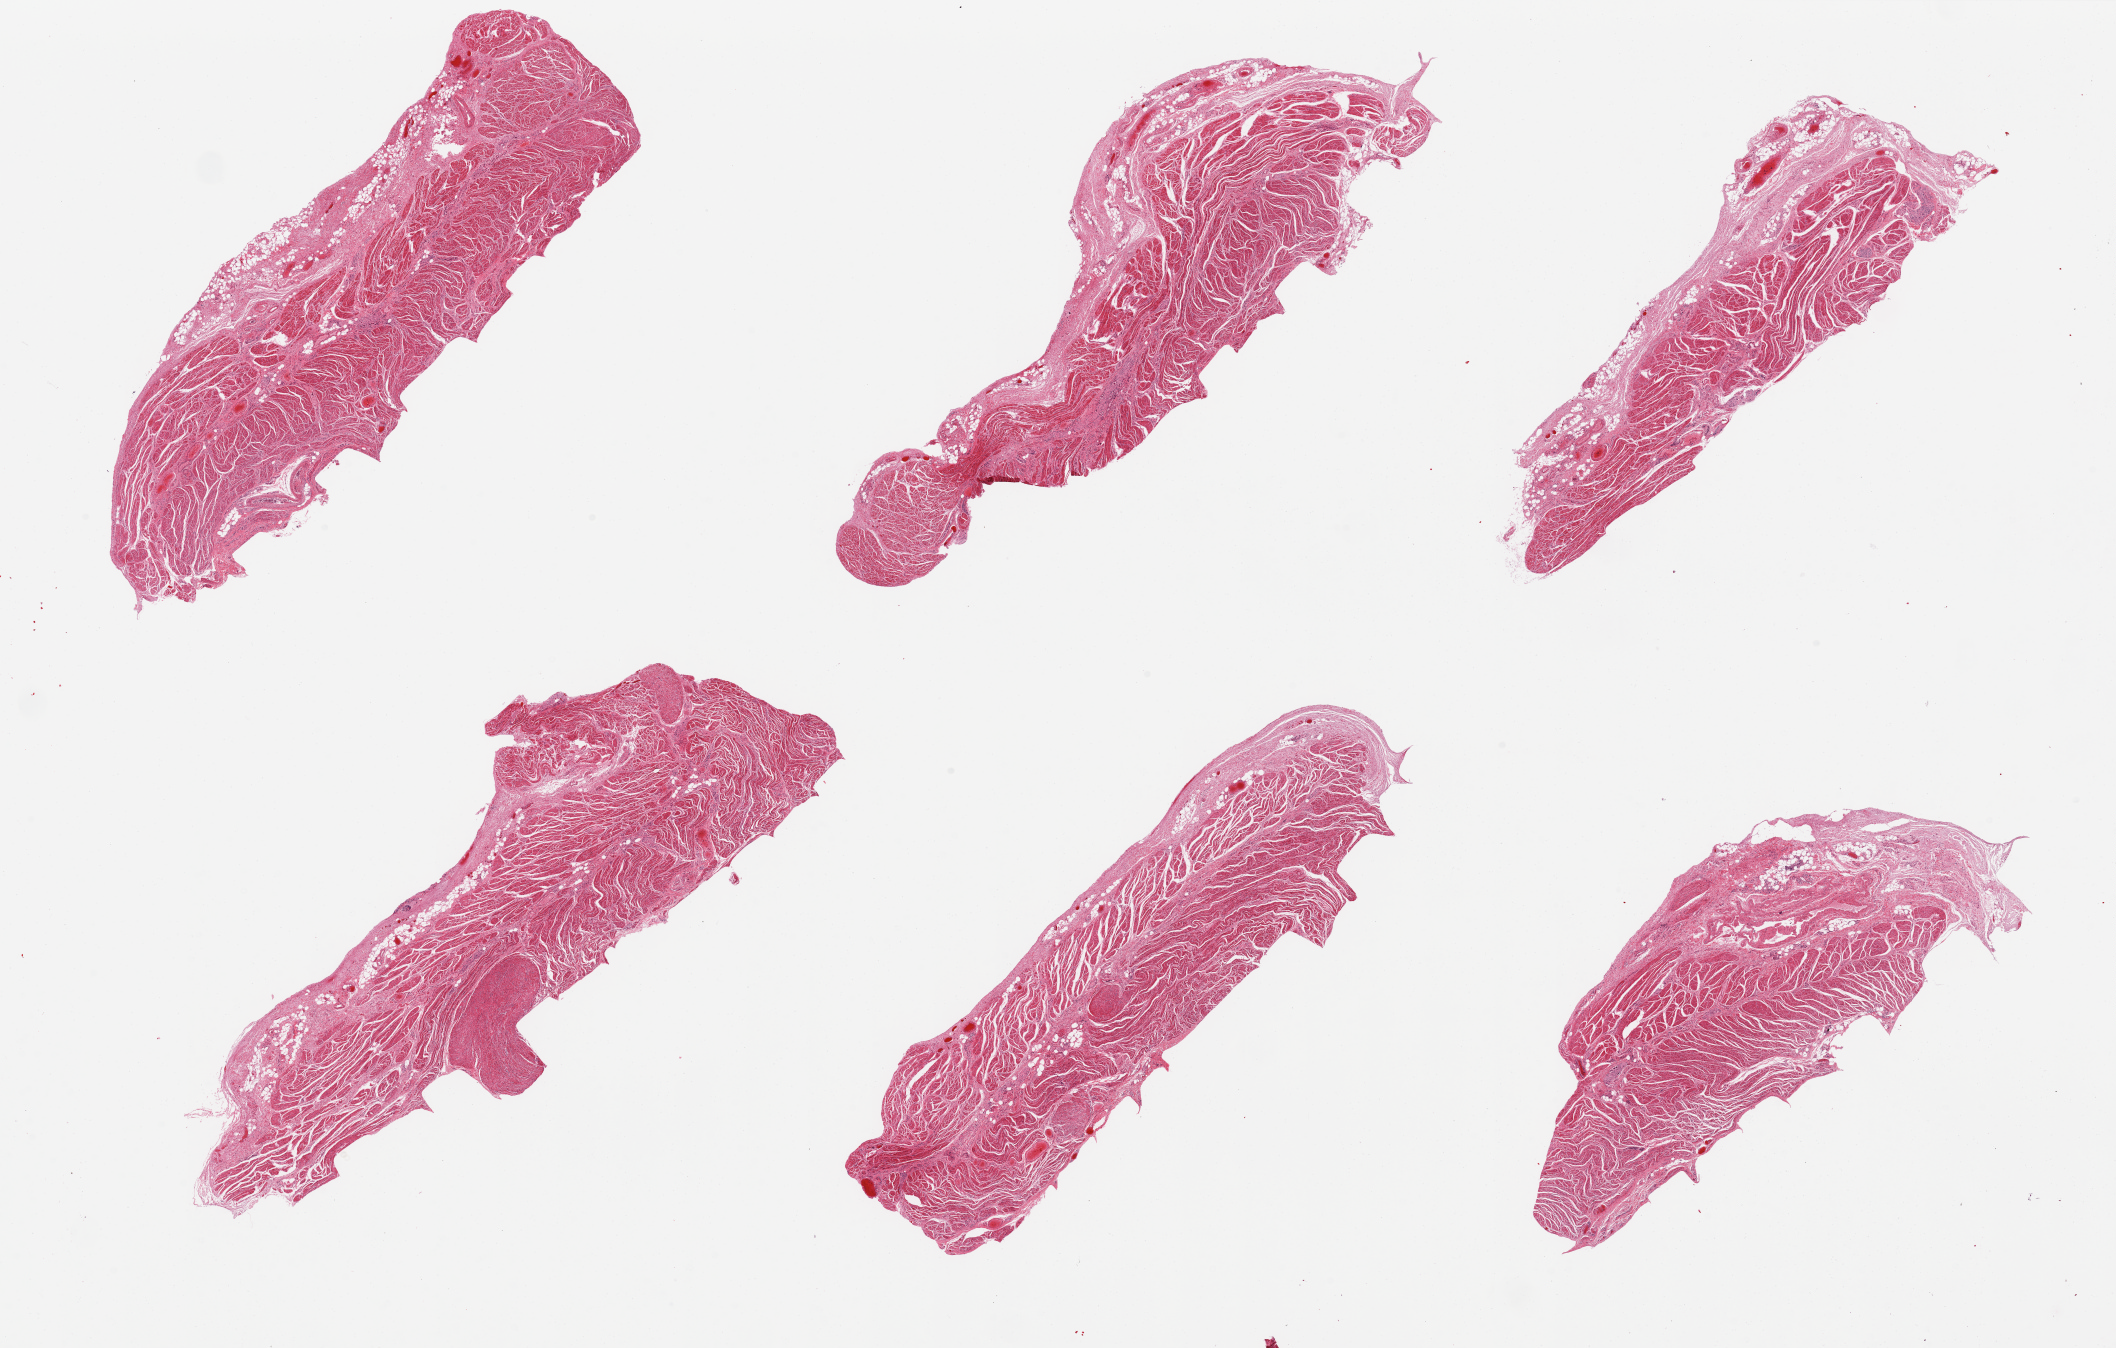
H&E whole-slide image, brightfield — low-resolution overview of the scanned area, about 33.5 x 21.3 mm, PAXgene-fixed paraffin-embedded (PFPE) section, target tissue: gastroesophageal junction, donor tissue sample. Donor: male.
Reviewer comment on this tissue sample: 6 pieces, all muscularis, good specimens.